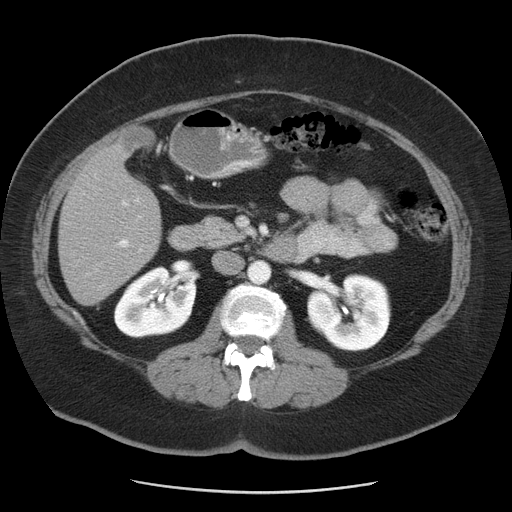
Contrast-enhanced abdominal CT, one axial slice; slice 19 of 55 in the series (ordered by position); reconstruction kernel STANDARD; 120 kVp; soft-tissue window (W 400 / L 40 HU); 5 mm slice thickness; 512 × 512 image matrix. Female patient, age 52 years. From the clinical record (not read from this slice): diagnosis: colorectal cancer liver metastases, imaged before liver resection; multiple liver metastases: yes; largest metastasis: 2.5 cm.
Structures marked on this image (outlined manually by an expert reader):
- liver: bounding box <59,125,162,306> (left, top, right, bottom; pixels)
- planned liver remnant (the part of the liver to remain after resection): <59,189,158,306>
- portal vein (with intrahepatic branches): <115,197,143,253>
- liver metastasis: <119,127,156,154>